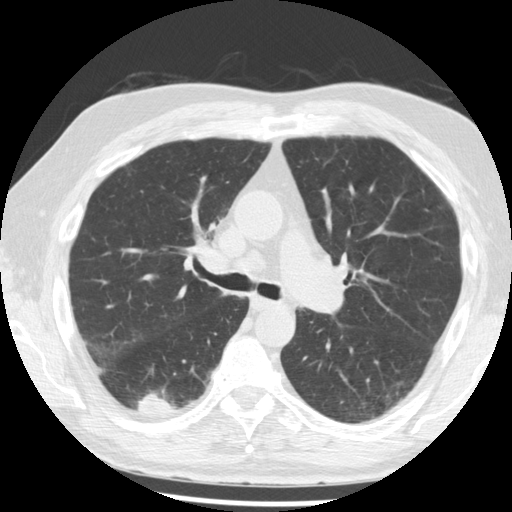
Low-dose screening chest CT, axial slice. Third annual screen. Lung window (W 1500 / L -600 HU). 2.5 mm slice thickness. Standard (soft-tissue) reconstruction kernel (STANDARD). Slice 131 of 221 in the series. 512 × 512 image matrix, field of view 350 × 350 mm. Male participant, aged 68 years at enrolment.
Expert-annotated lung lesion, bounding box <122,378,188,427> (left, top, right, bottom; pixels). The screening reader recorded 3 non-calcified nodules or masses ≥4 mm on this exam (right lower lobe, right lower lobe, right lower lobe); which of them this box marks is not recorded. Lung cancer was diagnosed 48 days after this screen: squamous cell carcinoma, NOS, right lower lobe, moderately differentiated (G2), stage IB (AJCC 6th edition), 20 mm at pathology.